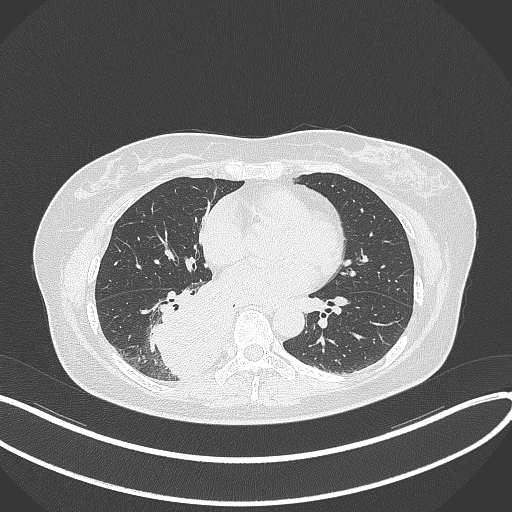
Chest CT, one axial slice; position 159 of 331 along the scan axis; reconstruction kernel B70f; lung window (W 1500 / L -600 HU); 1 mm slice thickness; 512 × 512 image matrix, field of view 400 × 400 mm. Patient: female, 54 years. Case-level facts recorded for this patient, not image findings: clinical TNM (as recorded): T4 N0 M0.
Annotated regions visible in this slice (bounding box drawn by a radiologist):
- lung tumour (recorded histology: adenocarcinoma): bounding box <147,284,227,377> (left, top, right, bottom; pixels)